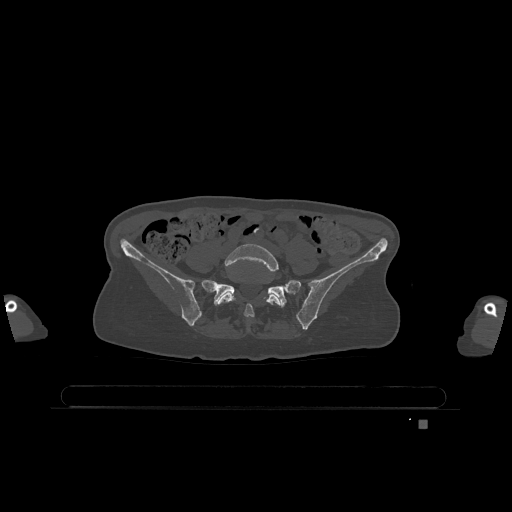
CT including the spine, one axial slice; slice 217 of 1317 in the series (ordered by position); bone window (W 1800 / L 400 HU); 512 × 512 image matrix, field of view 500 × 500 mm. Female patient, age 74 years. Case-level facts recorded for this patient, not image findings: primary cancer: lung; vertebrae with lytic lesions (as recorded): T1, T4, T5, T6, L4, L5.
Annotated regions visible in this slice (semi-automatic segmentation, software-assisted and operator-edited):
- L5 vertebra: bounding box [x1, y1, x2, y2] px = [217, 244, 281, 317]